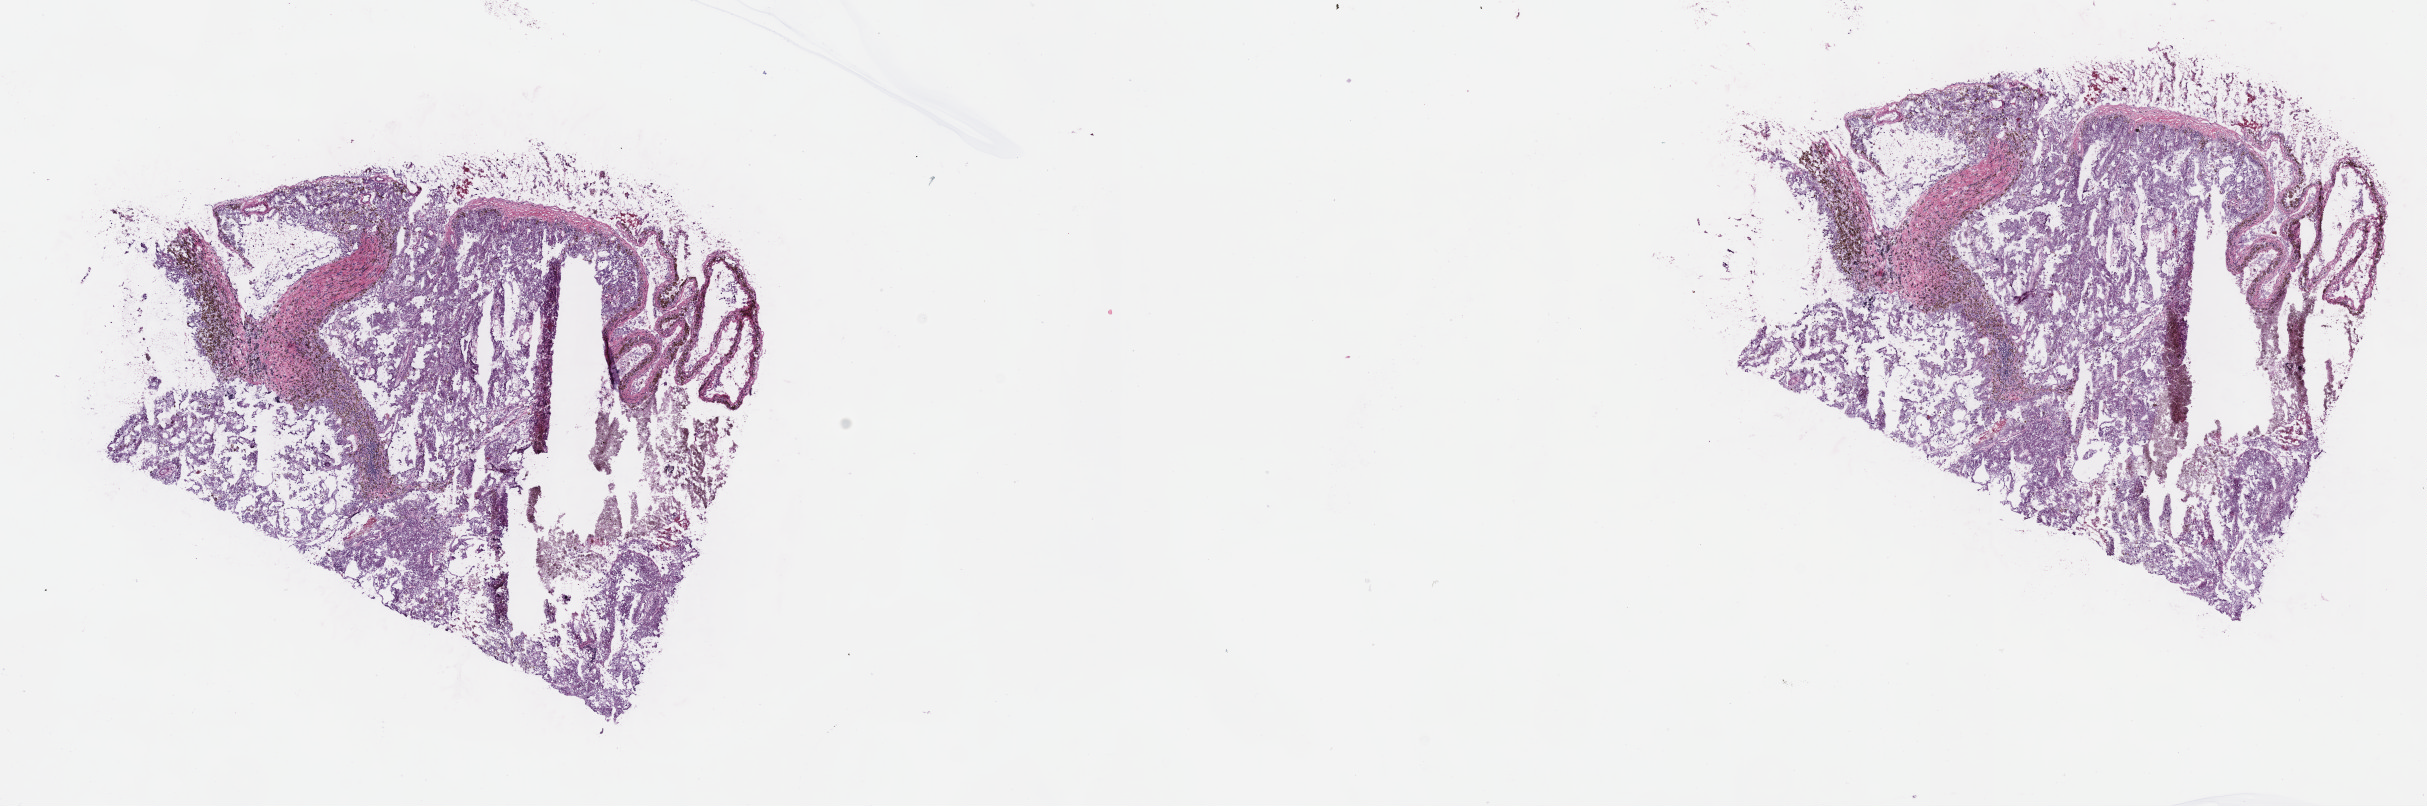
H&E whole-slide image, low-resolution overview of the scanned area, about 19.6 x 6.5 mm (slide scanned at 40x); frozen section from the top of the tissue portion; sample: primary tumour, kidney. Male, age 61 years at initial diagnosis. Composition of this section per pathologist review: tumour cells 50%, tumour nuclei 70%, normal cells 0%, stromal cells 37%, necrosis 13%. Inflammatory infiltration, as recorded: lymphocyte infiltration 3%, monocyte infiltration 20%, neutrophil infiltration 2%.
Pathologic diagnosis: Papillary adenocarcinoma, NOS. AJCC pathologic stage: I (7th edition). TNM: T1a NX MX.